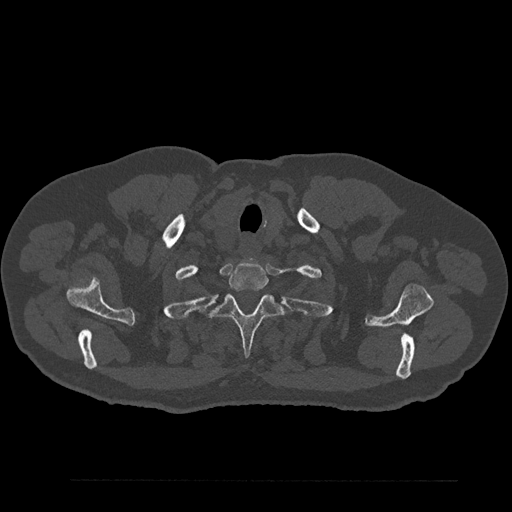
CT including the spine, one axial slice; slice 728 of 797 in the series (ordered by position); reconstruction kernel Br40s/3; 120 kVp; bone window (W 1800 / L 400 HU); 512 × 512 image matrix, field of view 430 × 430 mm. Male patient, age 61 years. From the clinical record (not read from this slice): primary cancer: prostate.
Annotated regions visible in this slice (semi-automatic segmentation, software-assisted and operator-edited):
- T1 vertebra: box from (x=228, y=262) to (x=268, y=291) px
- T2 vertebra: (x=212, y=294)–(x=289, y=356)